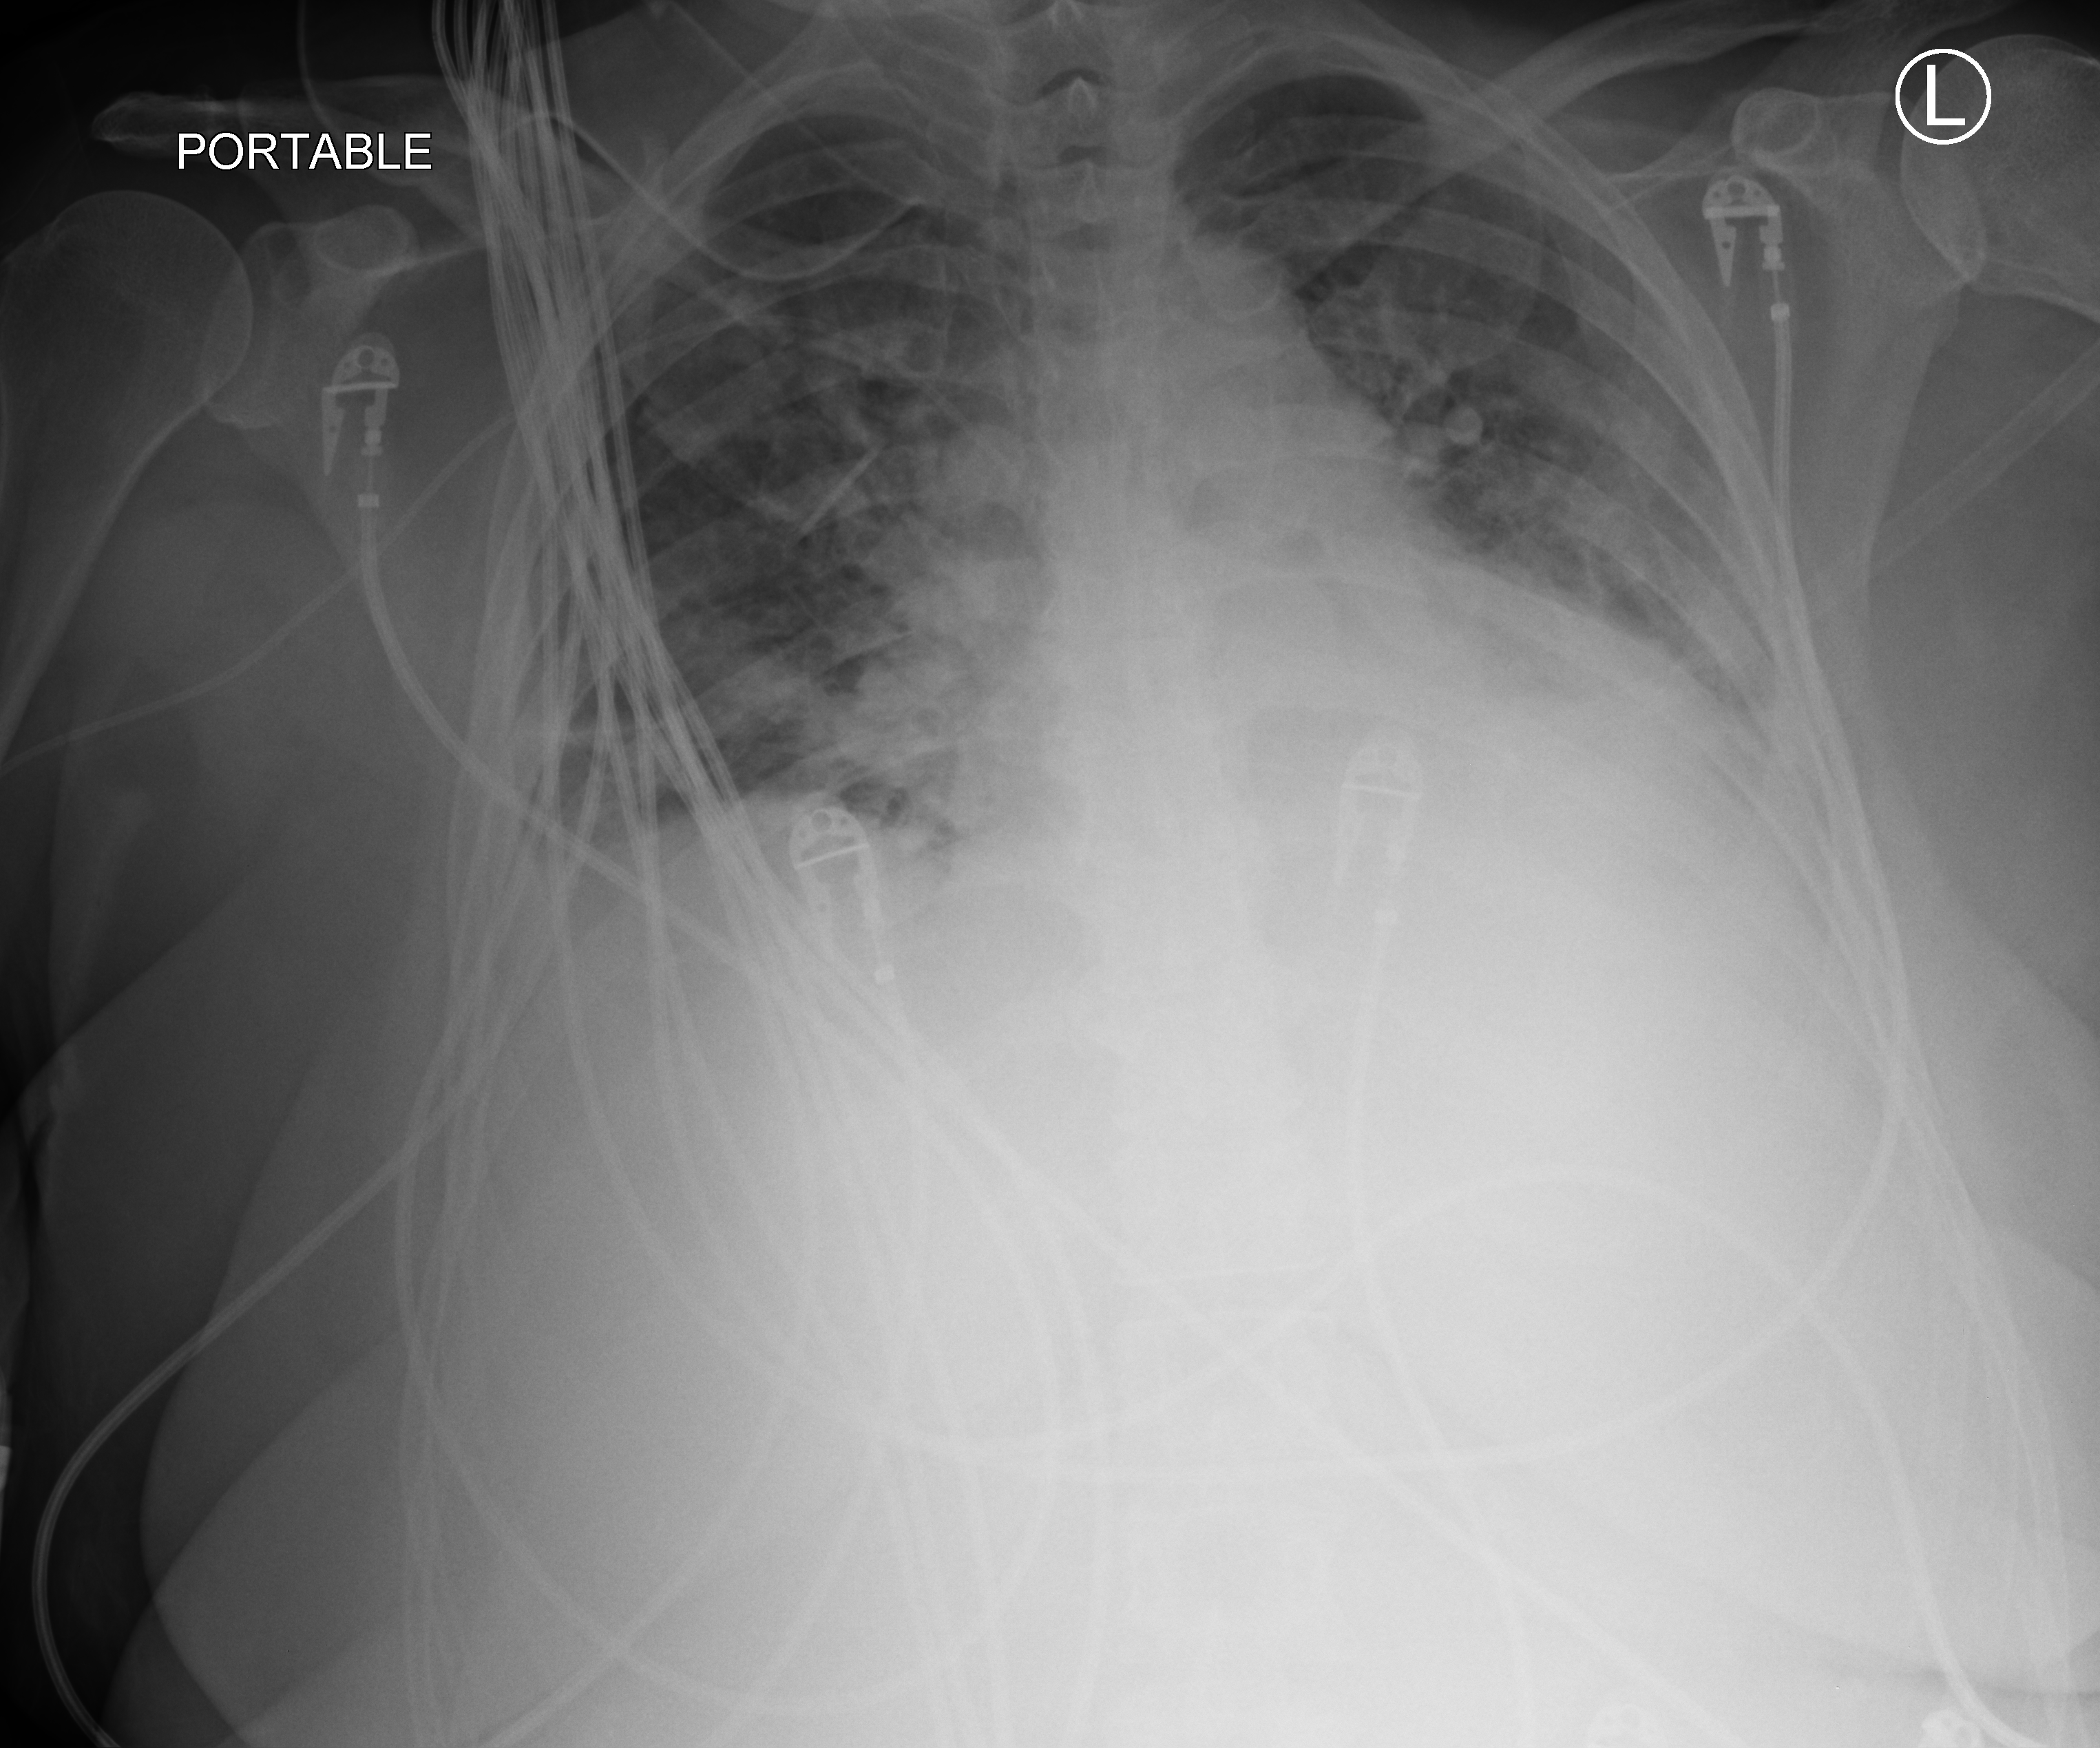
Bedside chest radiograph (computed radiography); anteroposterior (AP) projection. Female patient hospitalised with COVID-19, age 60–74 years.
From the hospital-stay record, not from the radiograph (when in the stay this image was taken is not recorded): admitted to intensive care during this hospital stay: yes.